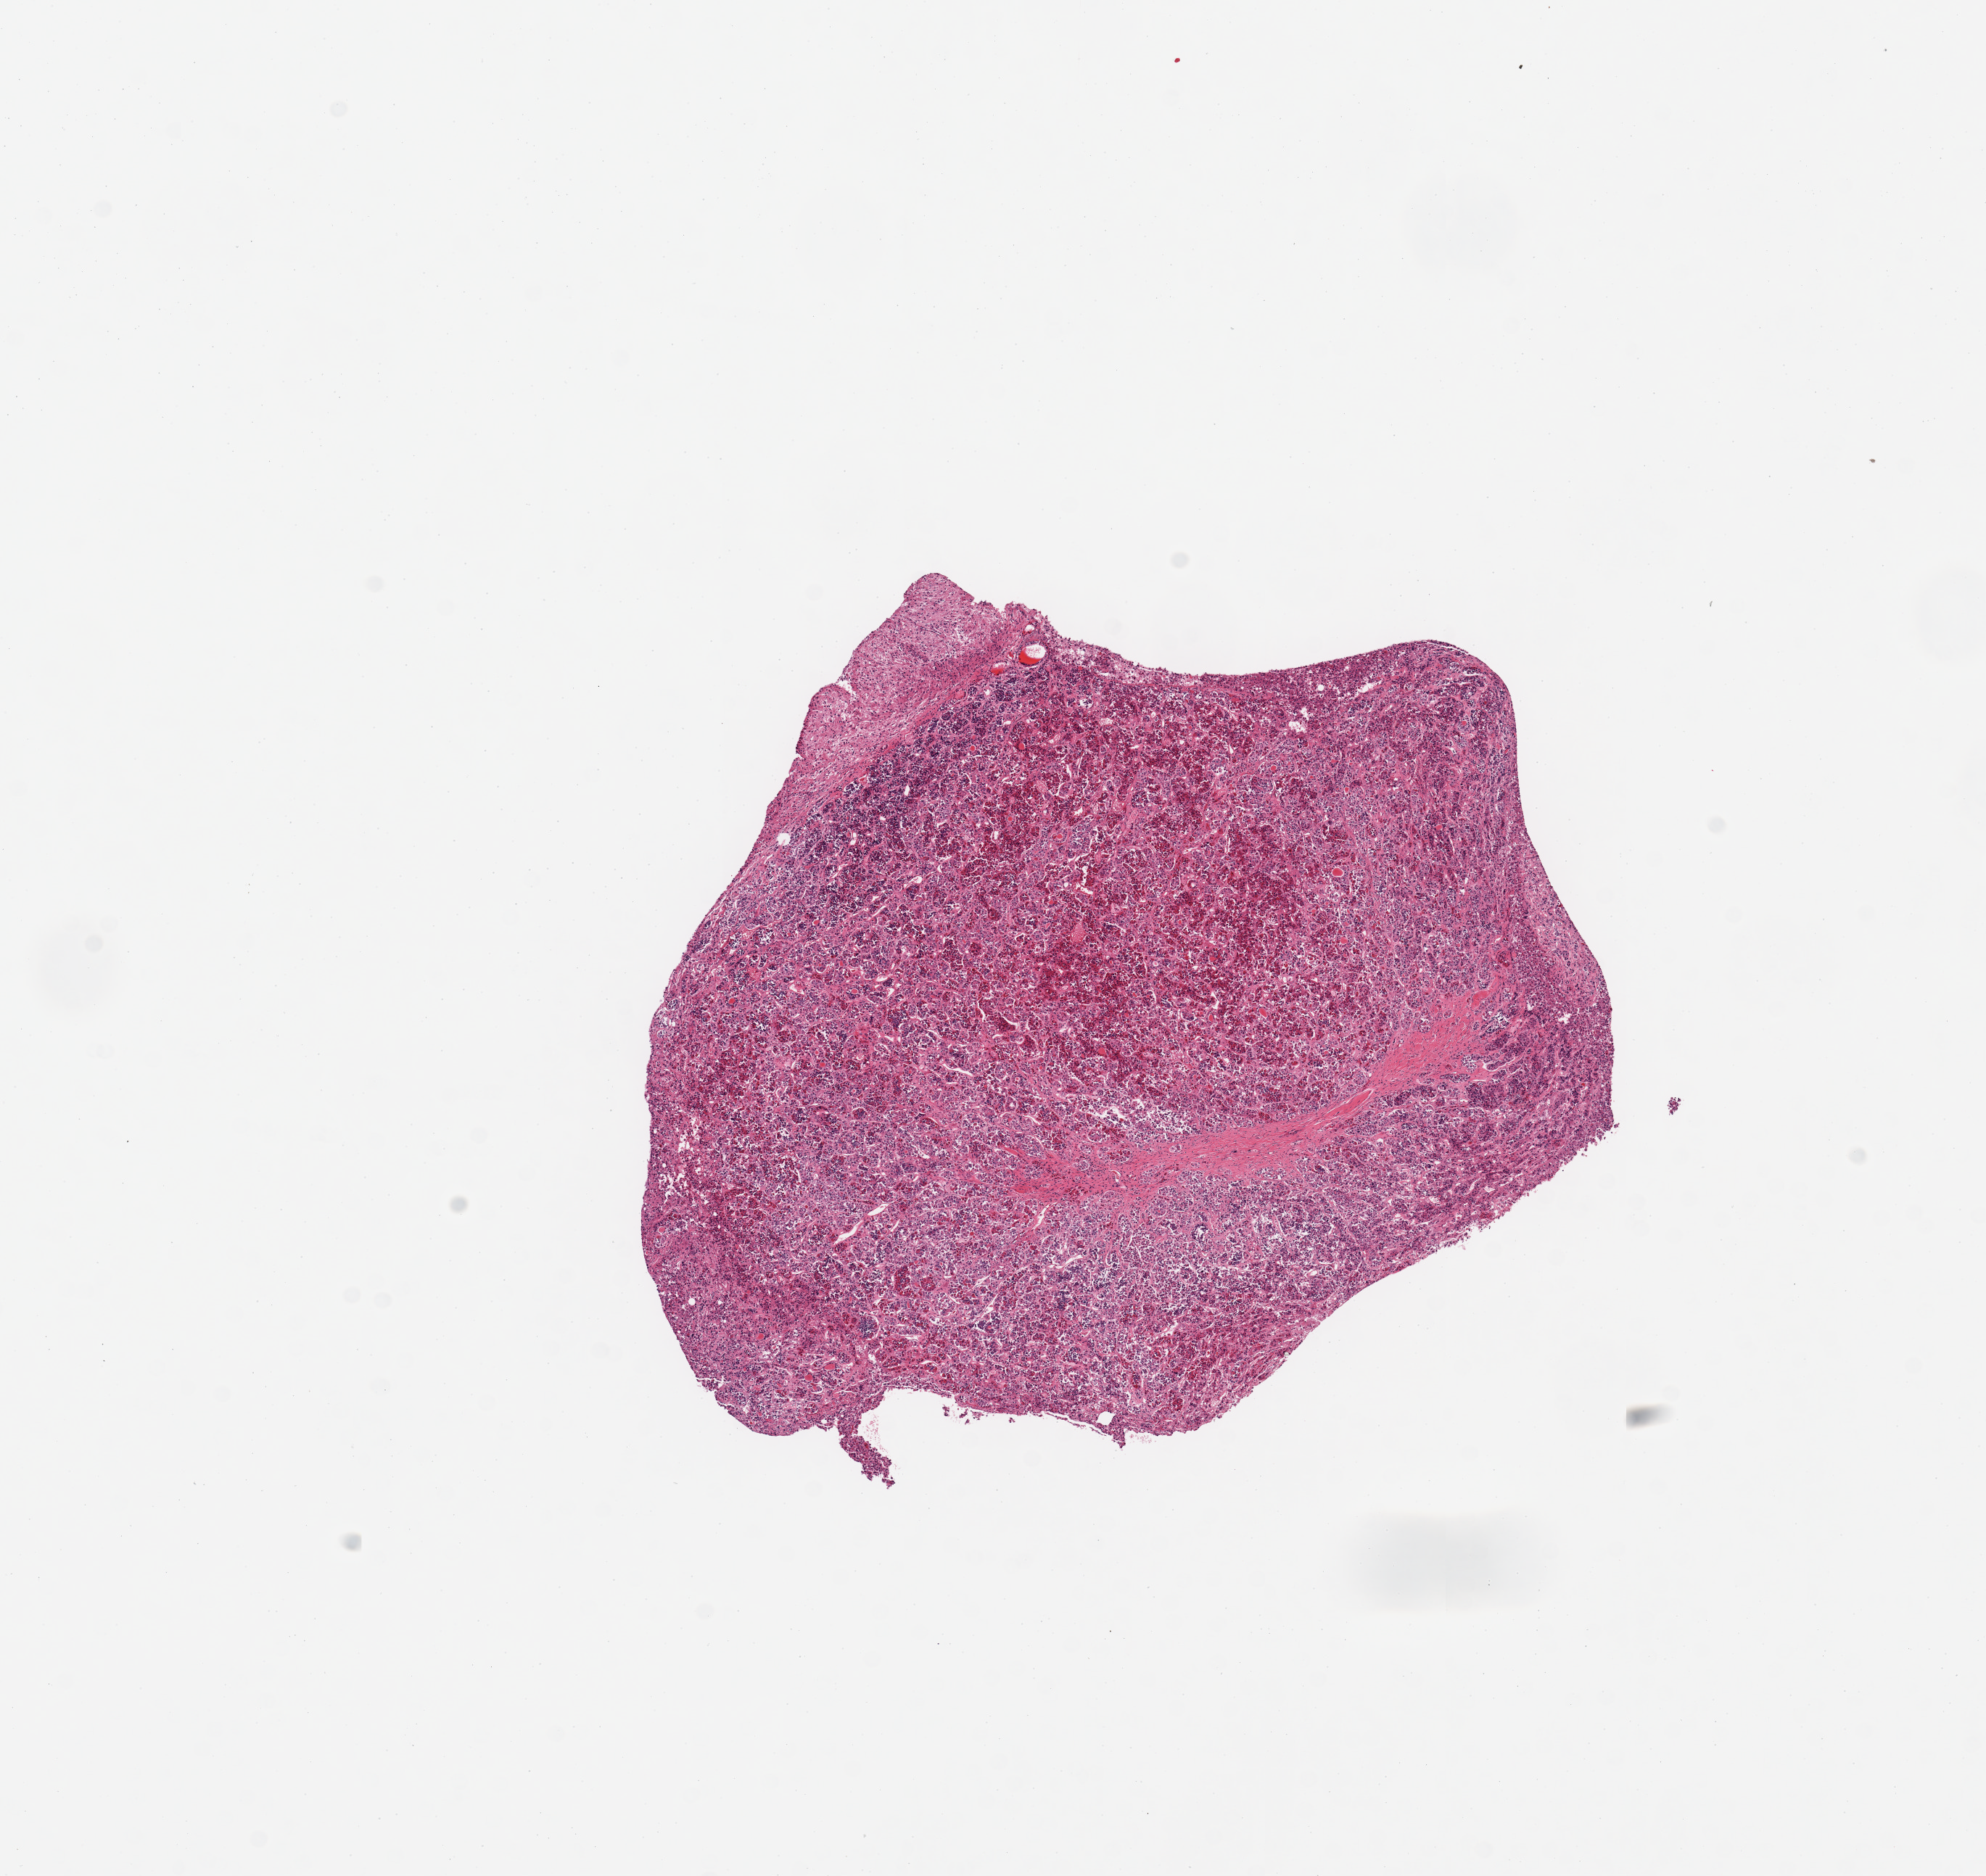
Digitized H&E-stained section — shown as a low-resolution overview of the whole scanned area (about 10.8 x 10.2 mm, acquisition: 20x scan). PAXgene-fixed, paraffin-embedded tissue. Section of pituitary (target tissue). Donor tissue sample. Donor: male.
* reviewer comment on this tissue sample: 1 piece; adenohypophysis ~90% and neurohypophysis ~10%